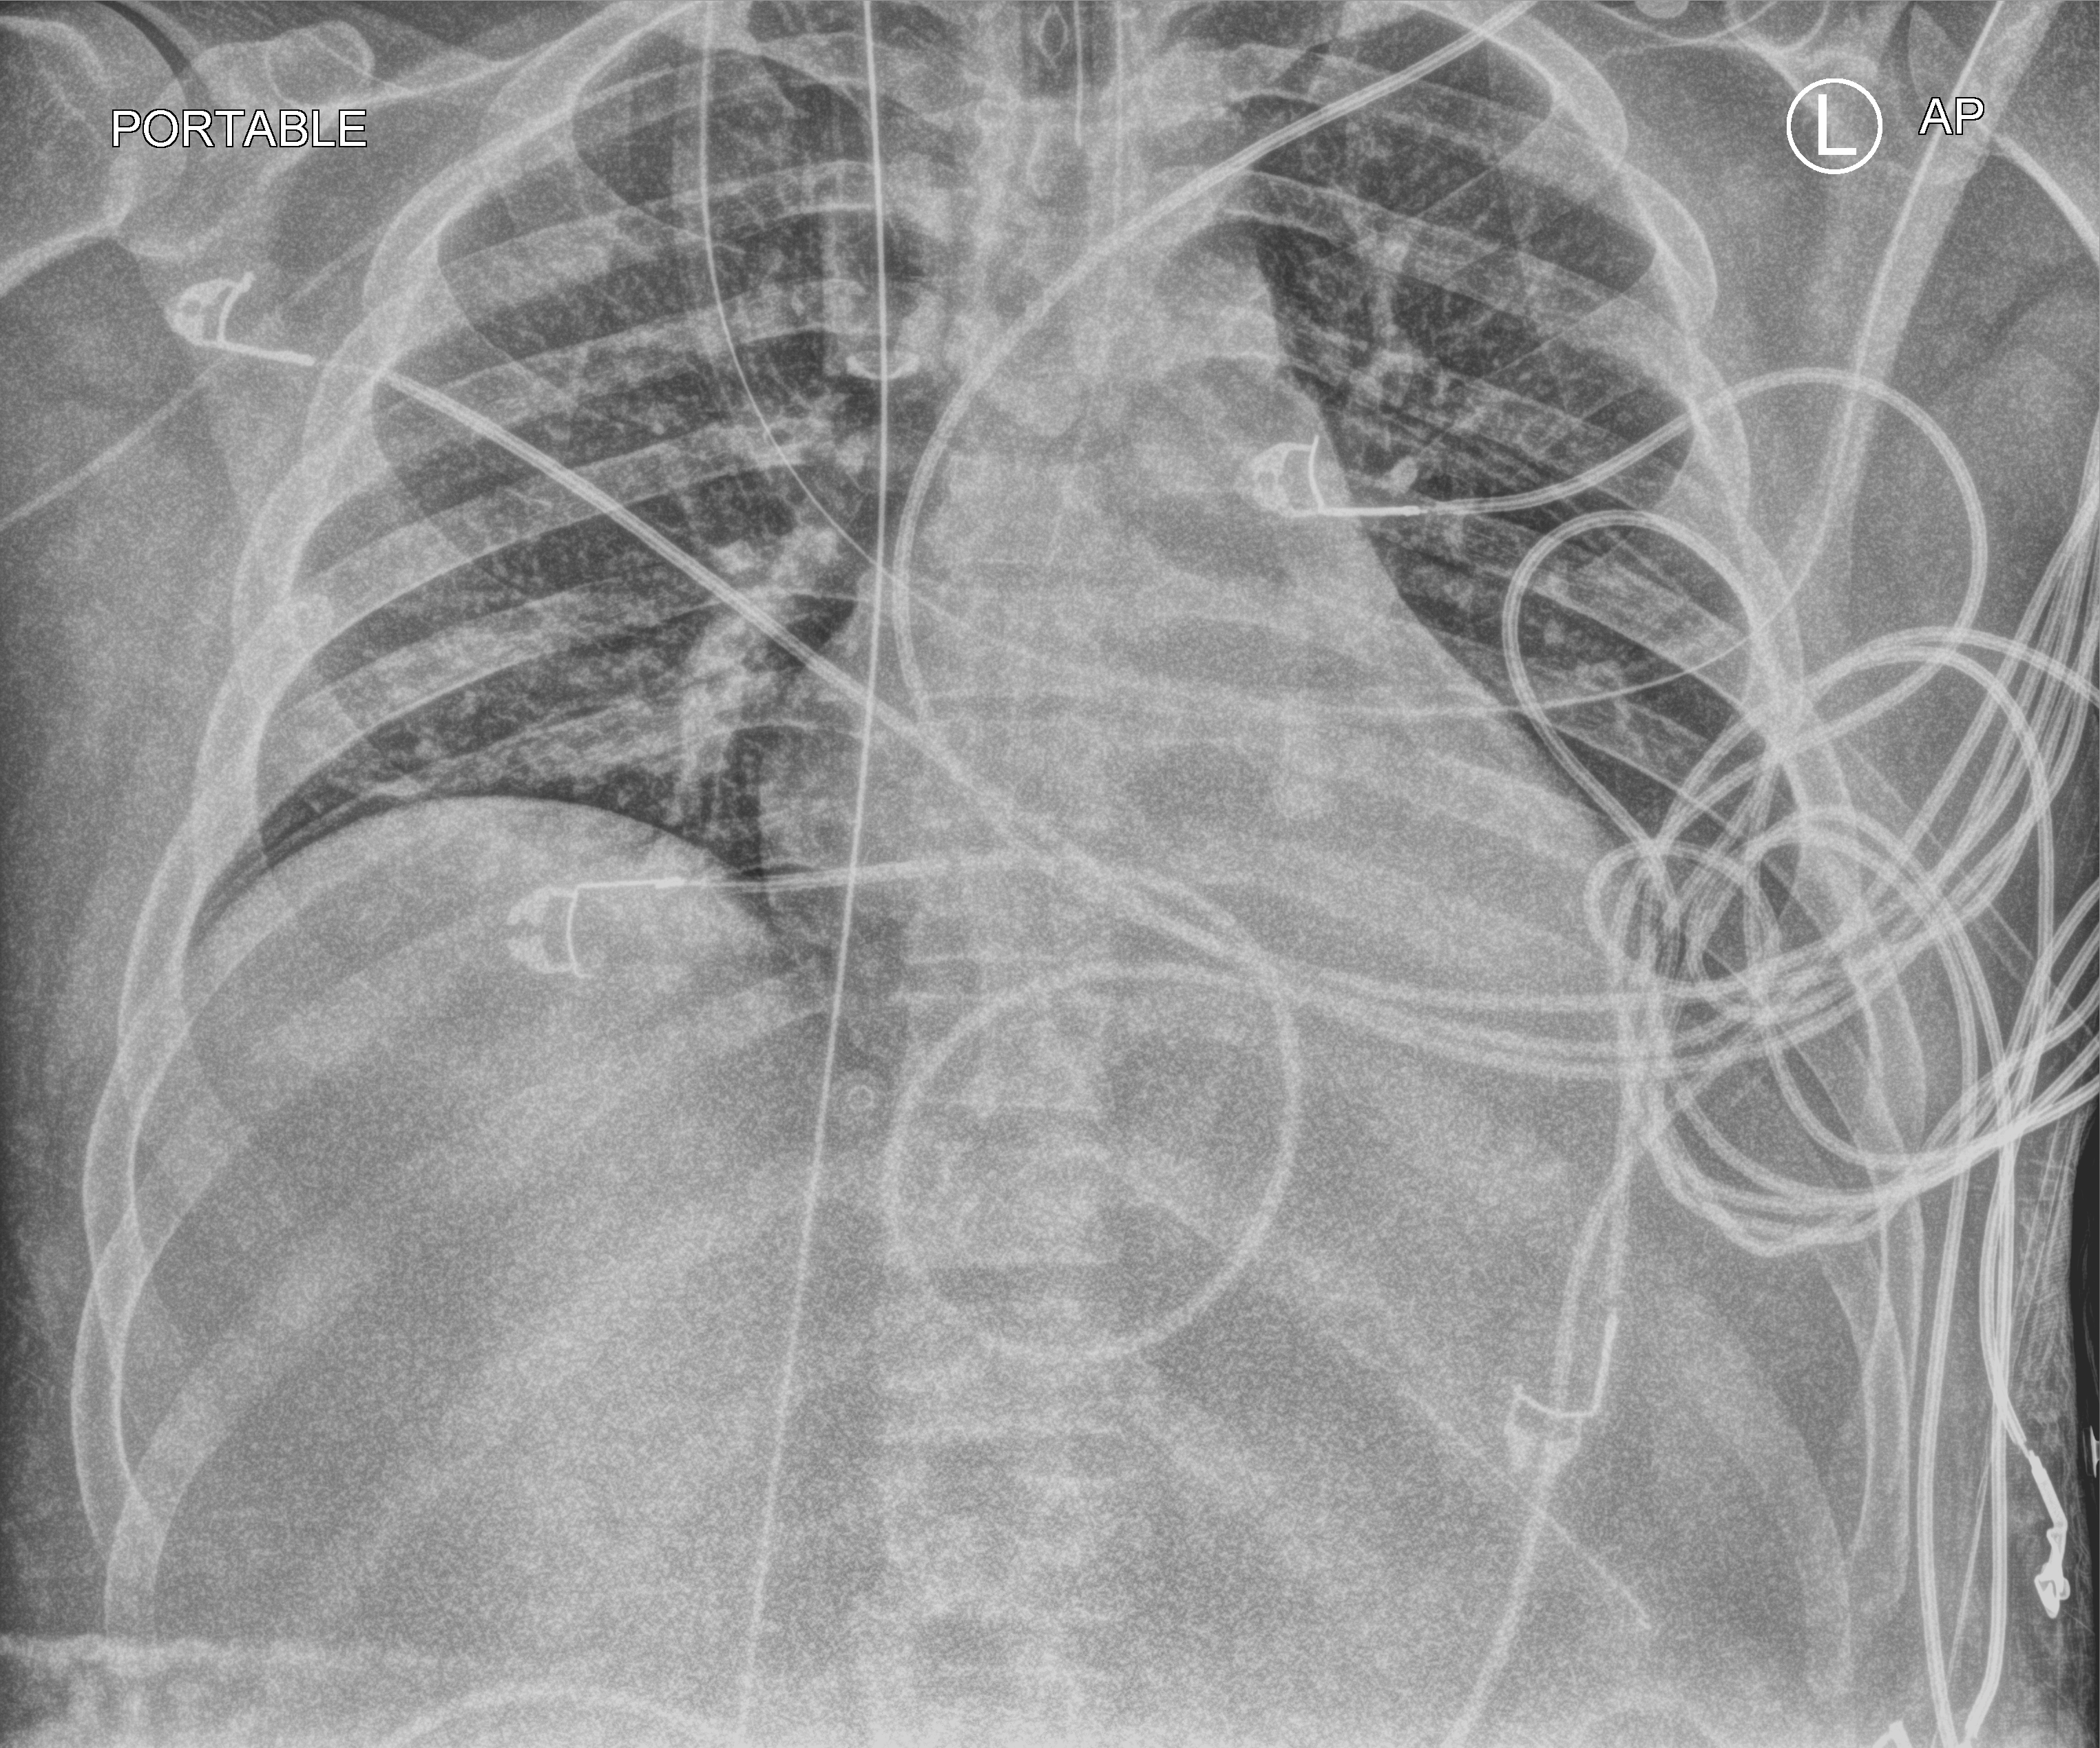
Portable chest radiograph. Male patient hospitalised with COVID-19, age 18–59 years.
Hospital-stay facts (about this admission, not read from this image; timing relative to this image not recorded): length of hospital stay: 61 days; admitted to intensive care during this hospital stay: yes.